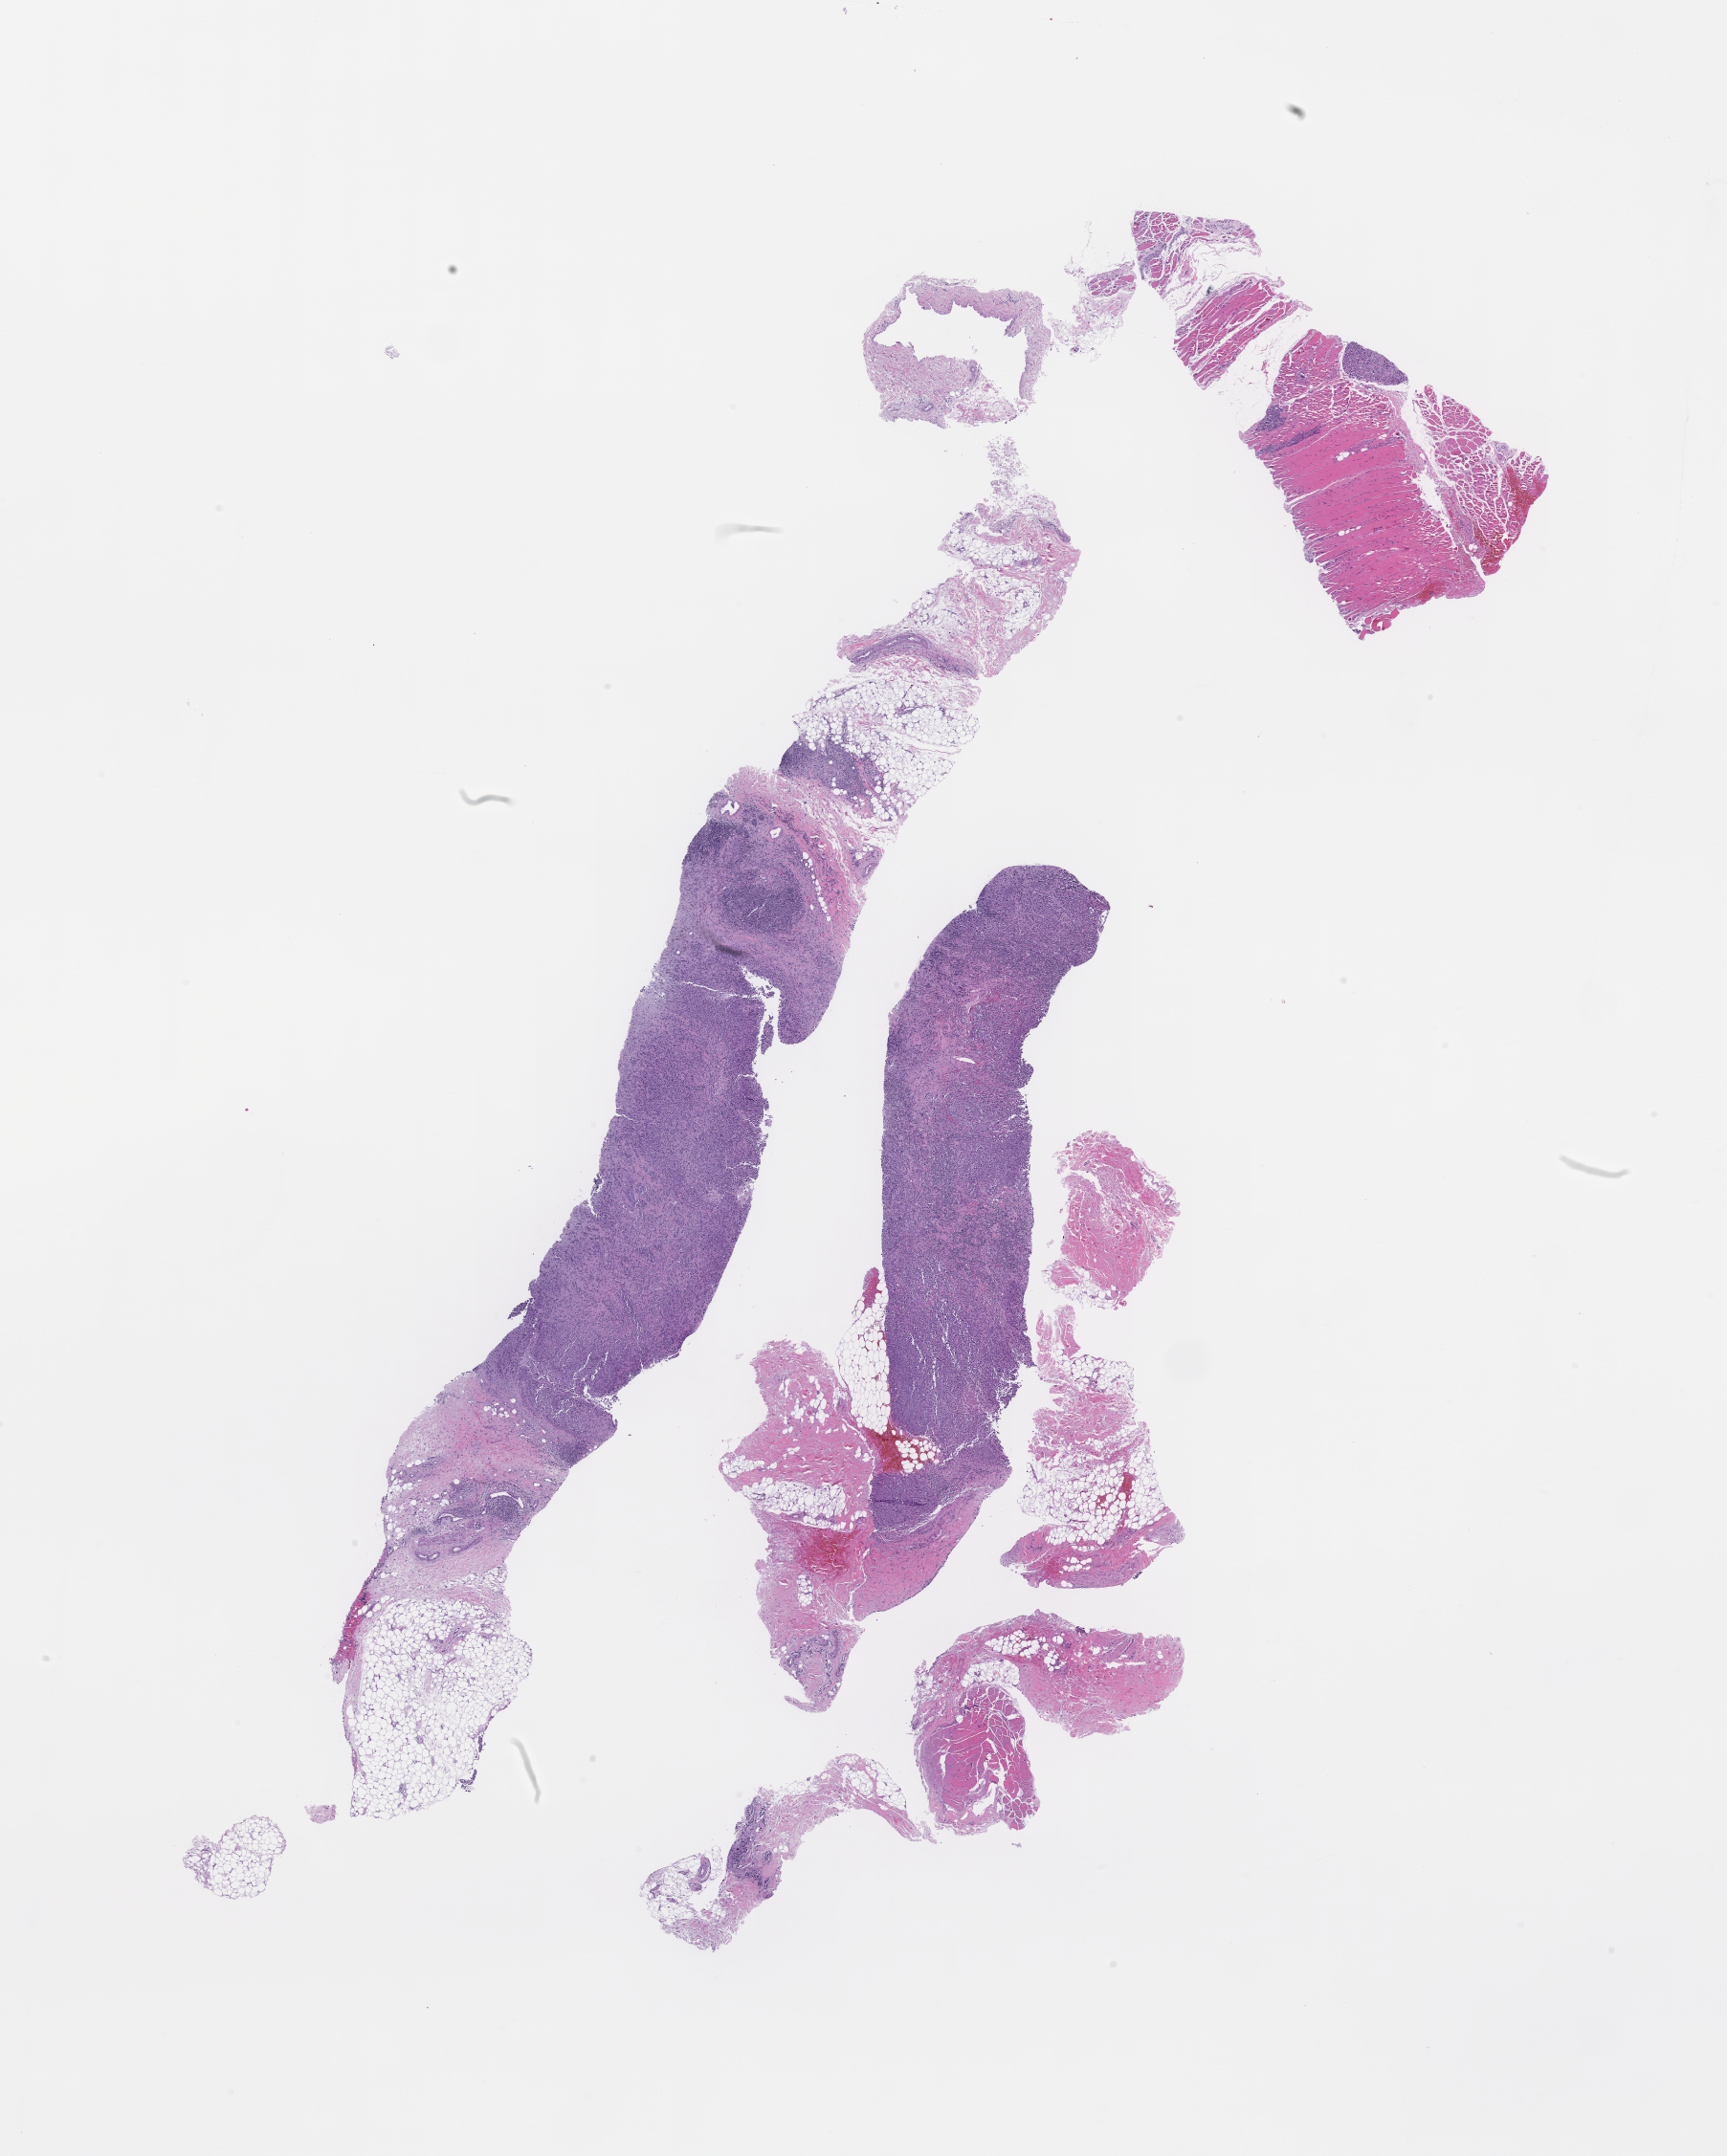
Haematoxylin and eosin whole-slide image — whole scanned area (about 14.6 x 18.2 mm) shown as a low-resolution overview. Formalin-fixed paraffin-embedded section. Archival tissue. Patient: male.
- this section: metastatic tumor tissue
- primary diagnosis of the patient: Melanoma